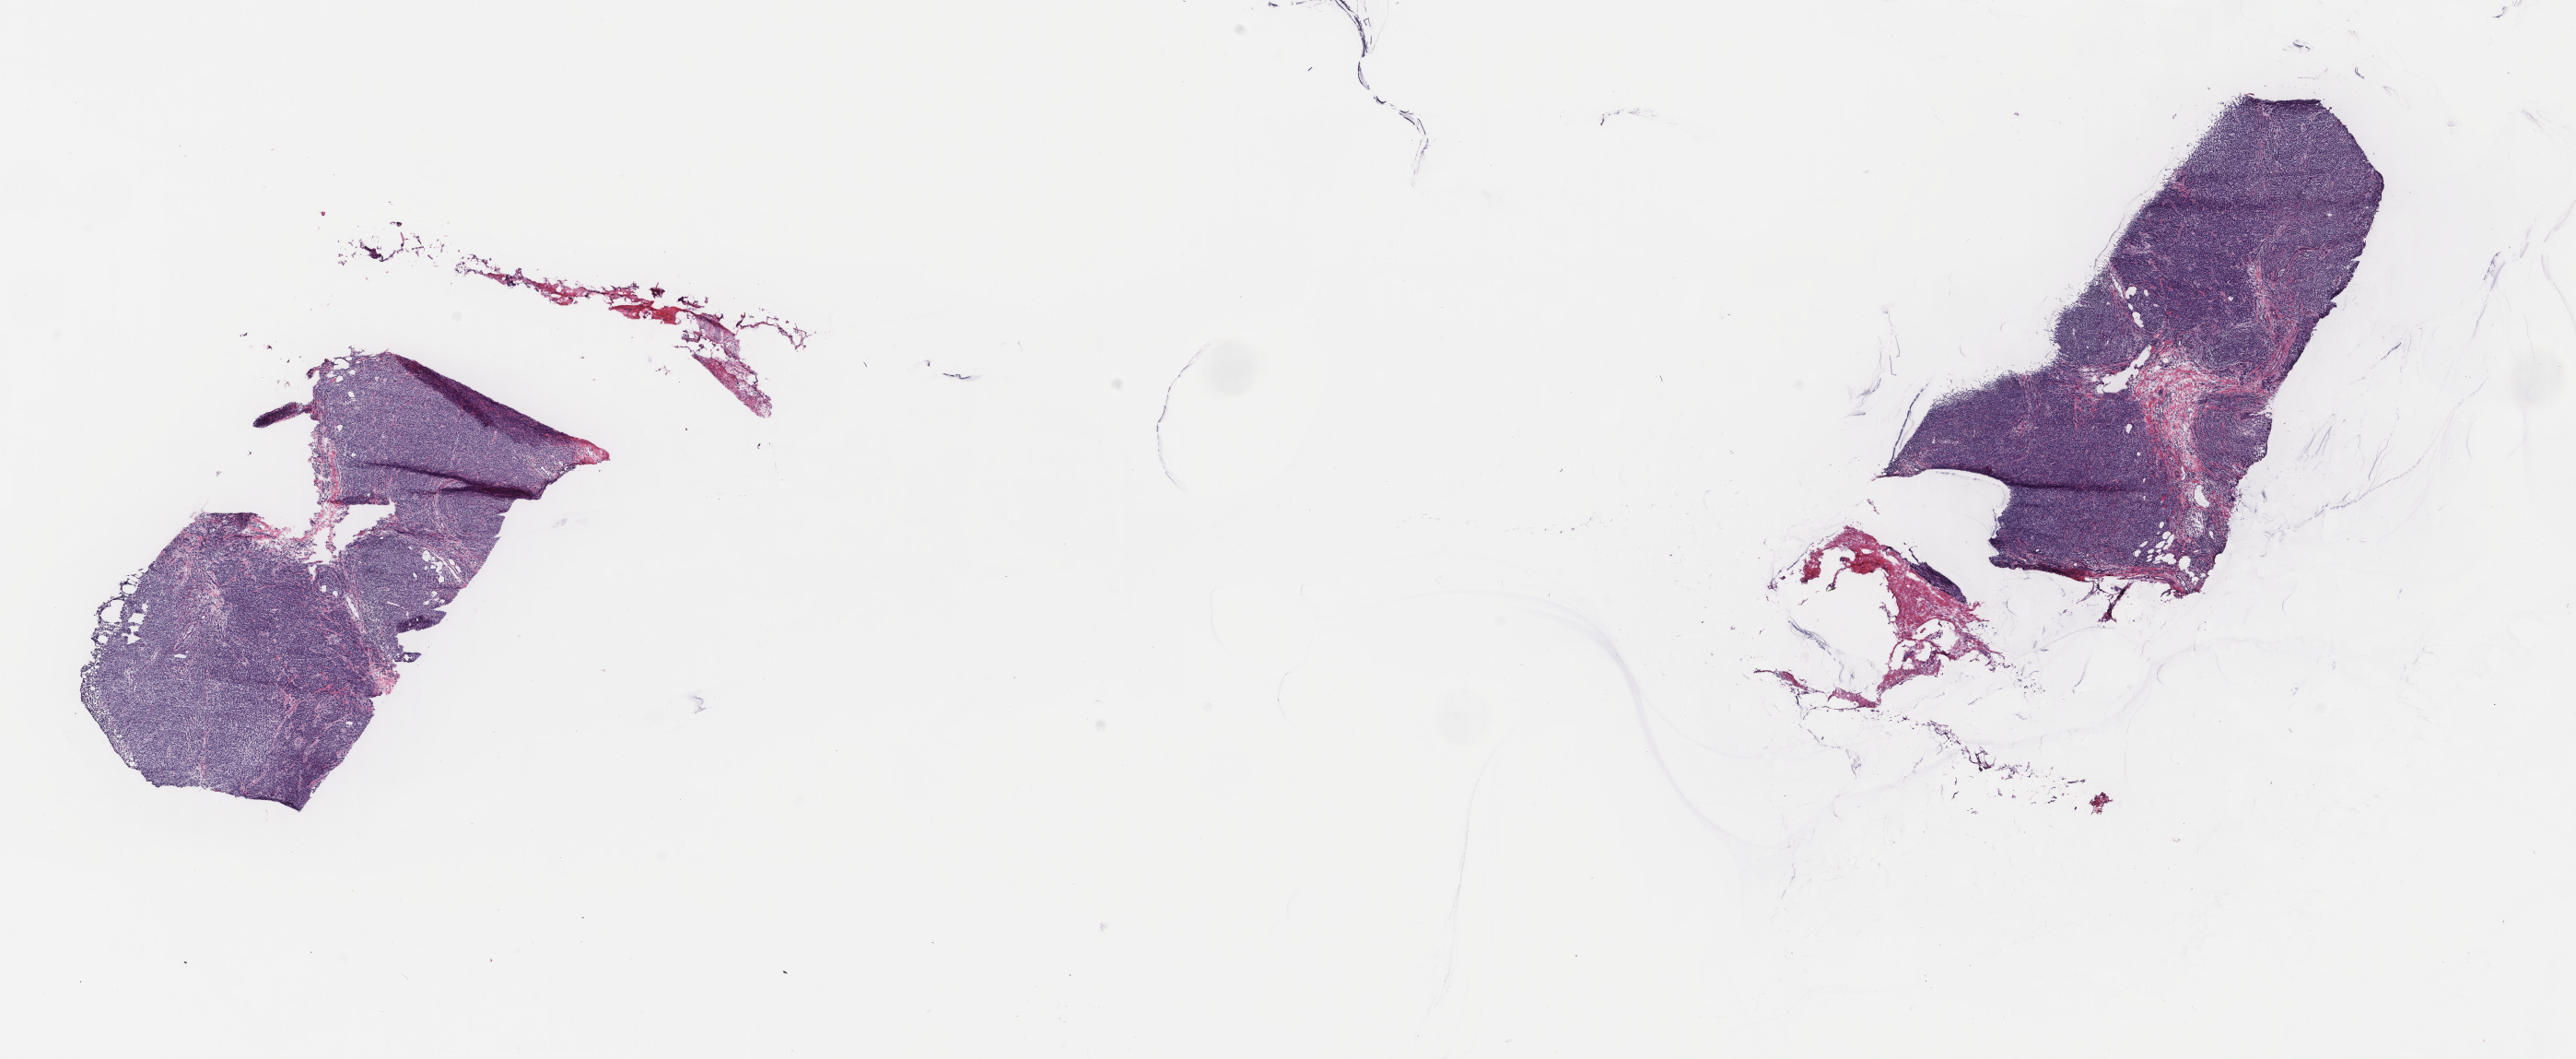
Hematoxylin and eosin (H&E) stained whole-slide image — whole scanned area (about 22.2 x 9.1 mm, acquisition: 40x scan) shown as a low-resolution overview; frozen section from the top of the tissue portion; sample: primary tumour, breast. Female, age 56 years at initial diagnosis. Pathologist review of this section (percent, as recorded): tumour cells 80%, tumour nuclei 80%, normal cells 0%, stromal cells 19%, necrosis 1%. Inflammatory infiltration, as recorded: lymphocyte infiltration 3%, monocyte infiltration 1%, neutrophil infiltration 1%.
Pathologic diagnosis: Lobular carcinoma, NOS. AJCC pathologic stage: IIA. Lymph nodes positive (case pathology): 0 of 3 examined.